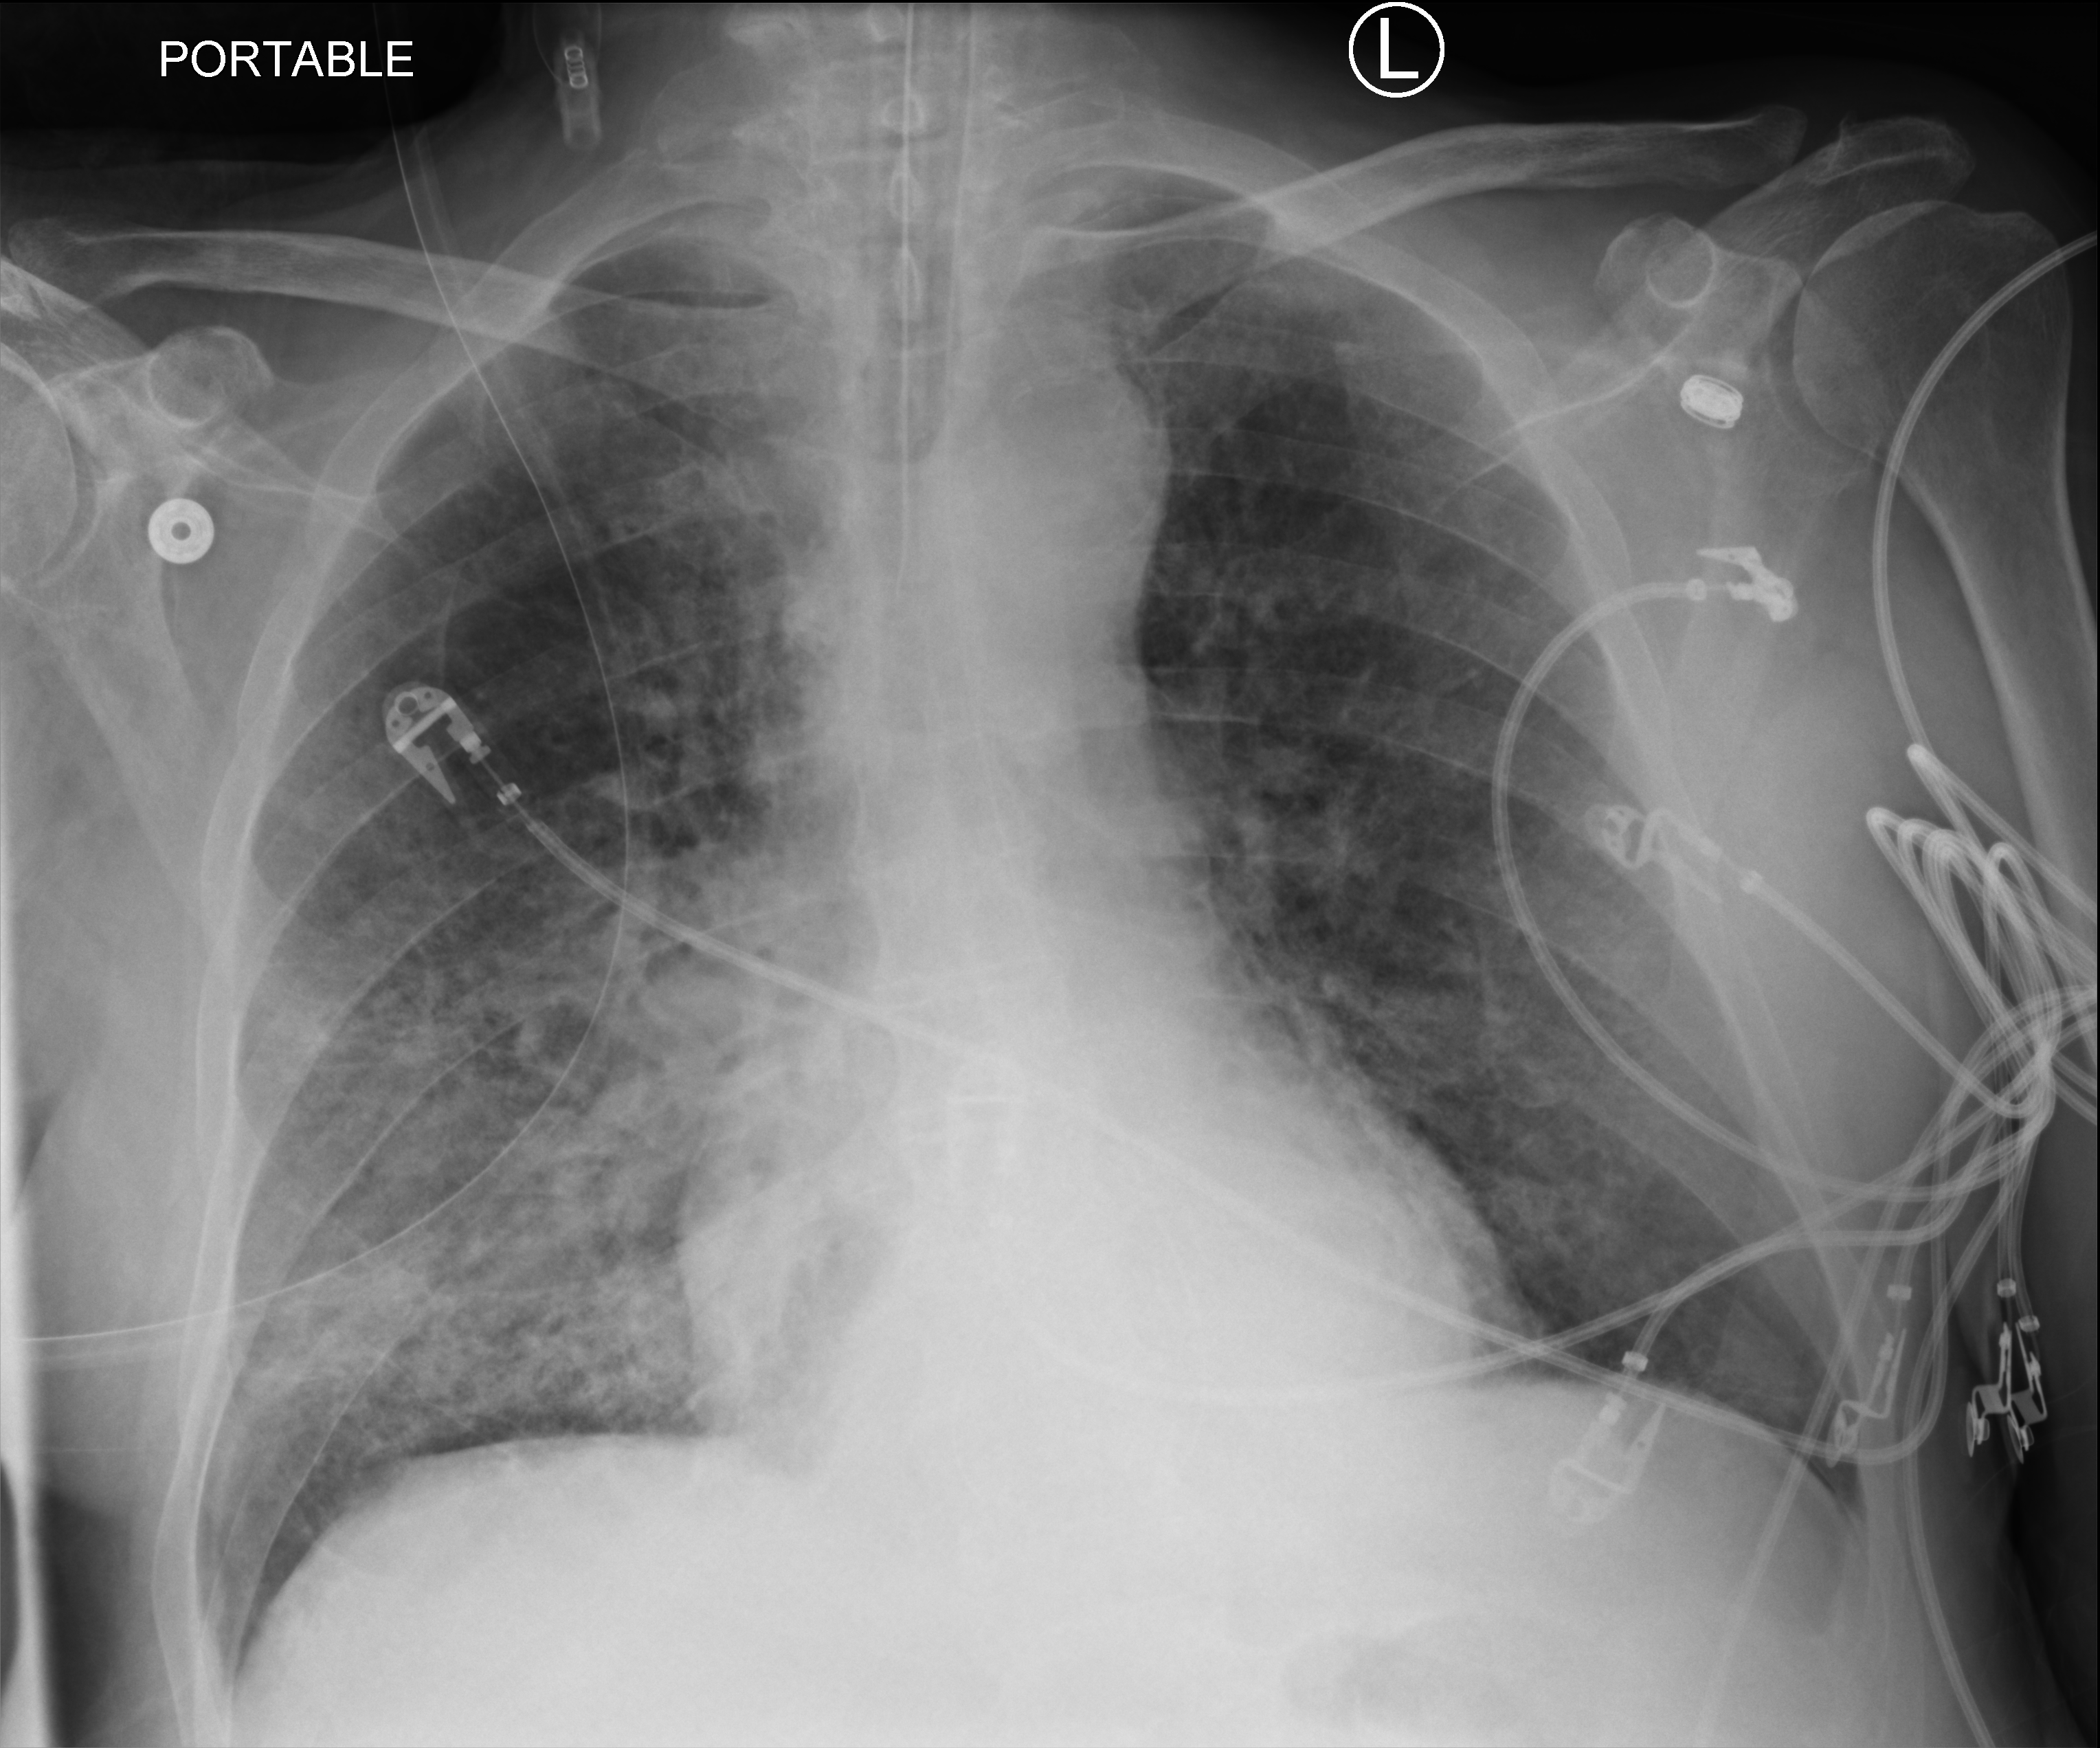
Chest X-ray (portable). Male patient hospitalised with COVID-19, age 75–90 years.
From the hospital-stay record, not from the radiograph (when in the stay this image was taken is not recorded):
- mechanically ventilated during this hospital stay: yes
- COPD (admission record): no
- length of hospital stay: 10 days